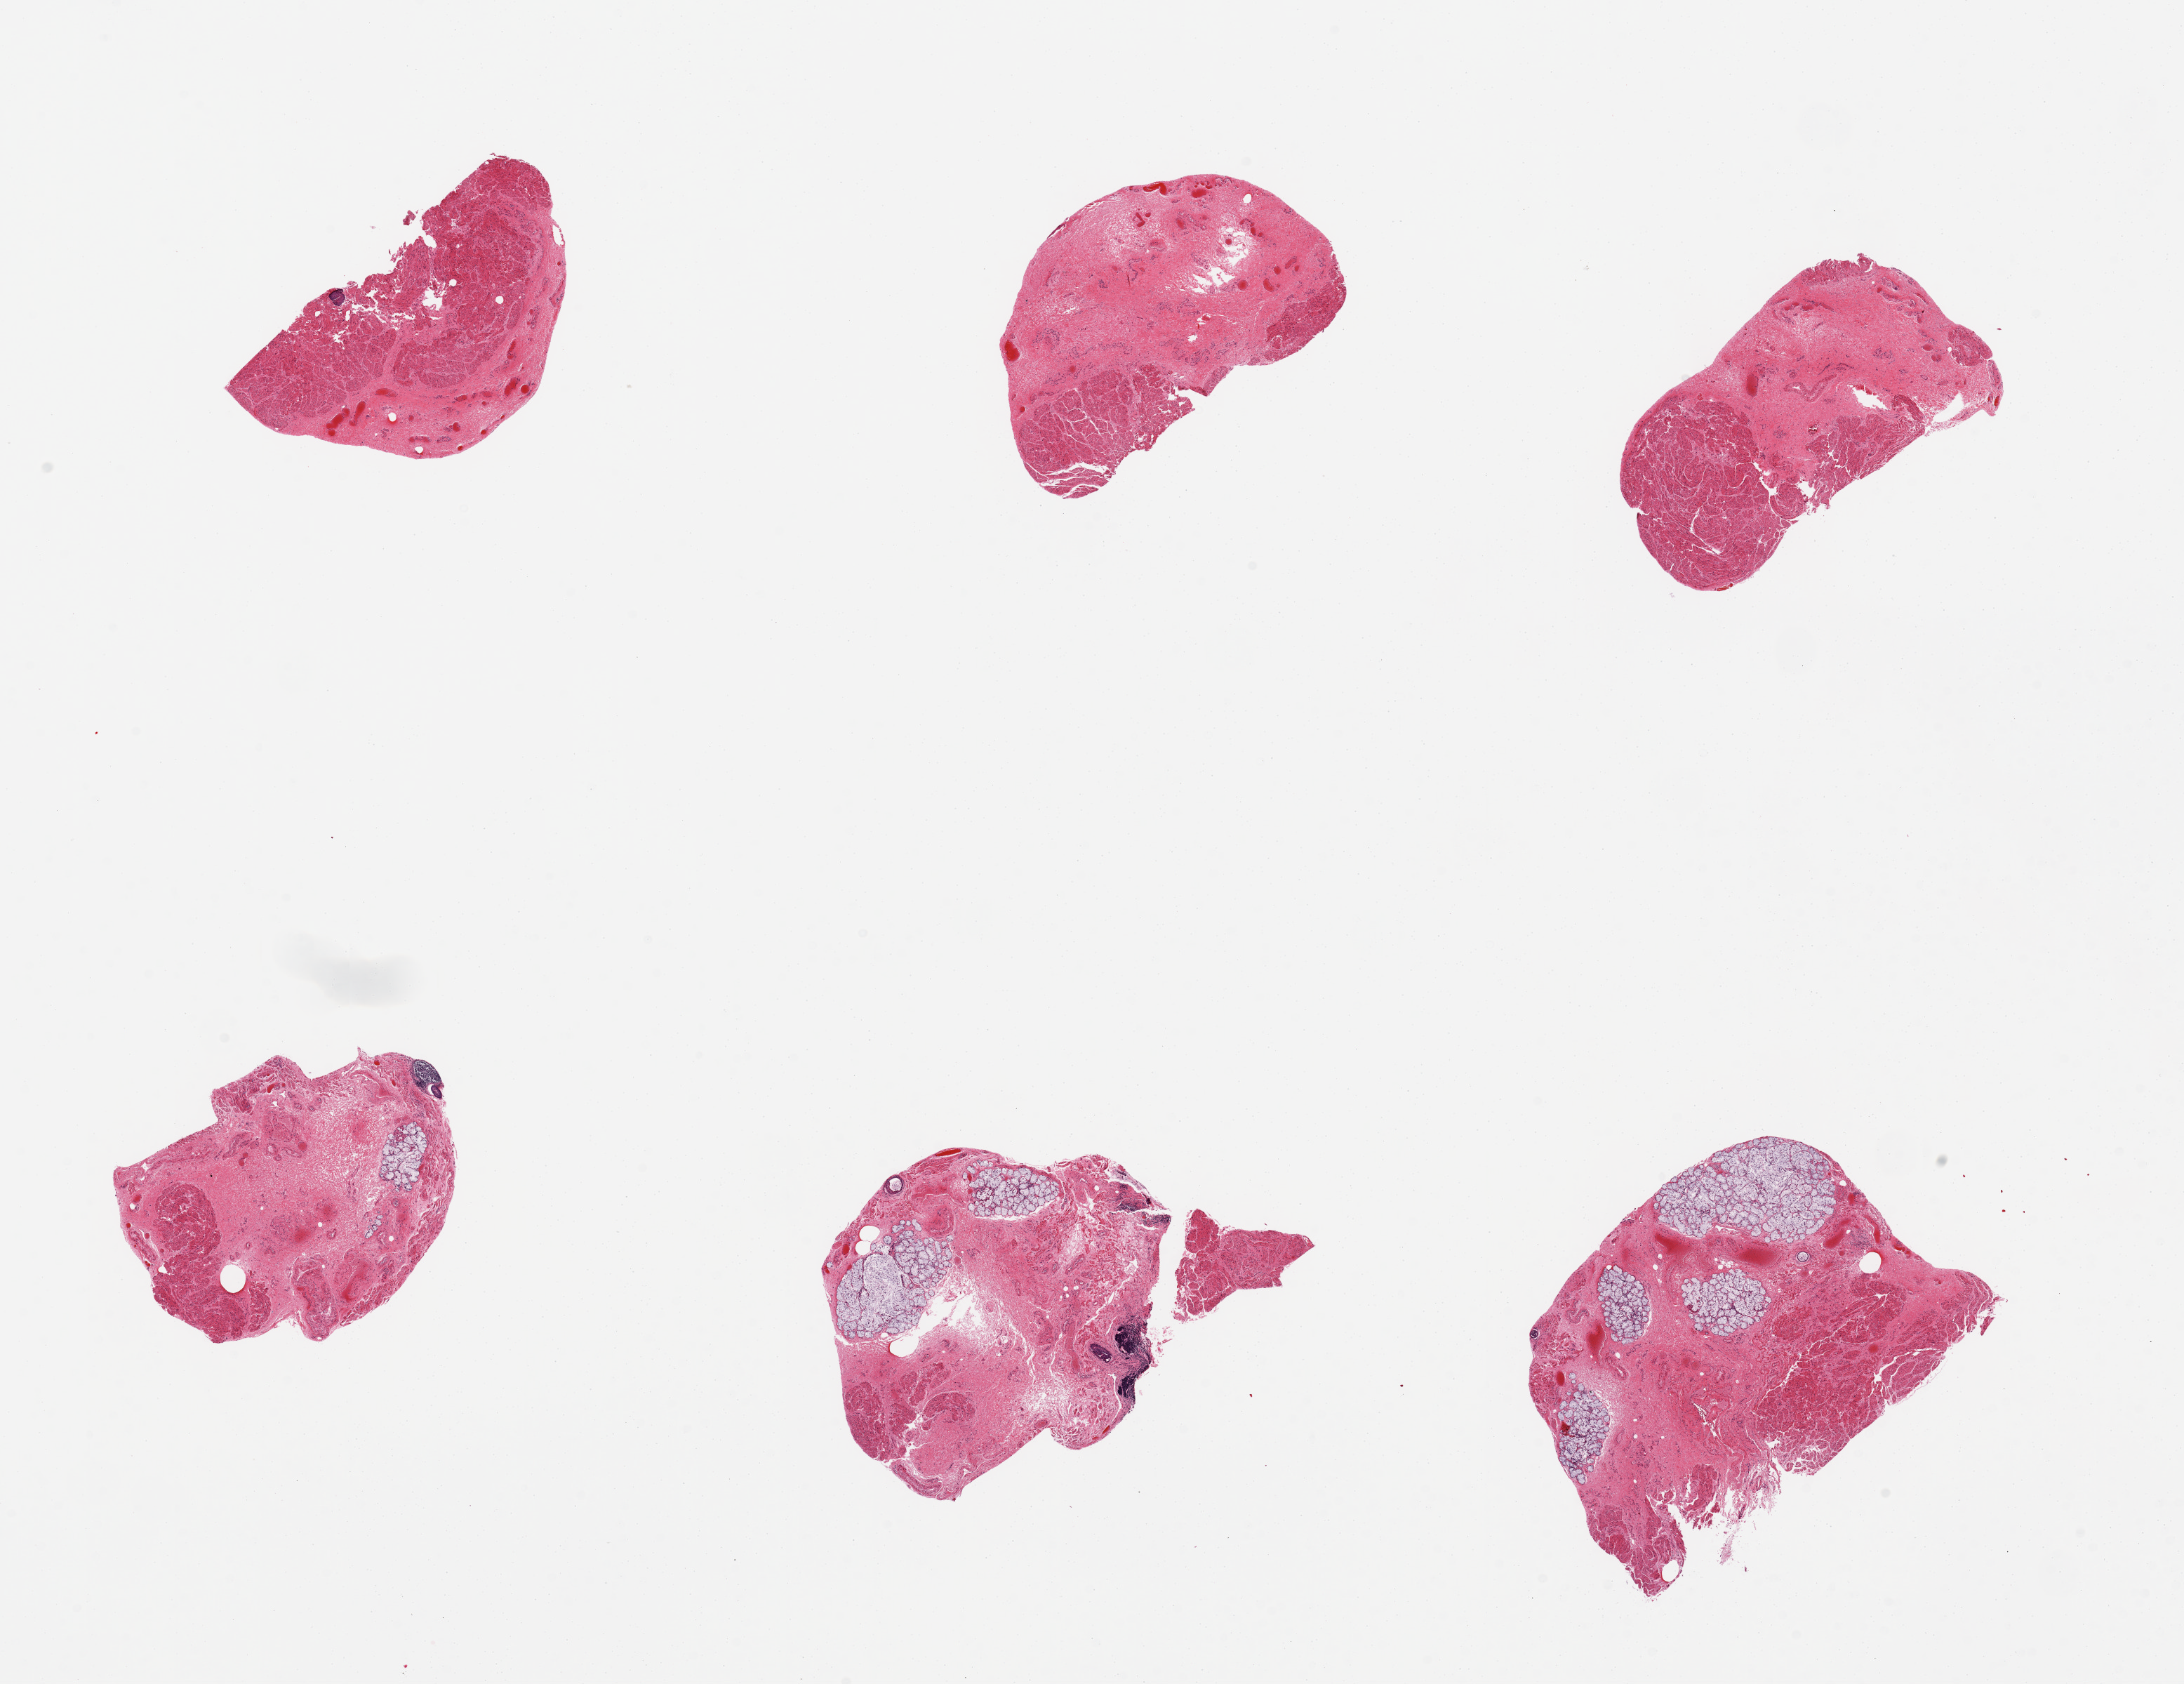
Hematoxylin and eosin (H&E) whole-slide image, whole scanned area (about 24.6 x 19.0 mm) shown as a low-resolution overview, PAXgene-fixed, paraffin-embedded tissue, target tissue: esophageal muscle, donor tissue sample. Male donor.
Pathologist's review note for this sample: 6 pieces, includes abundant submucosa and submucosal glands.